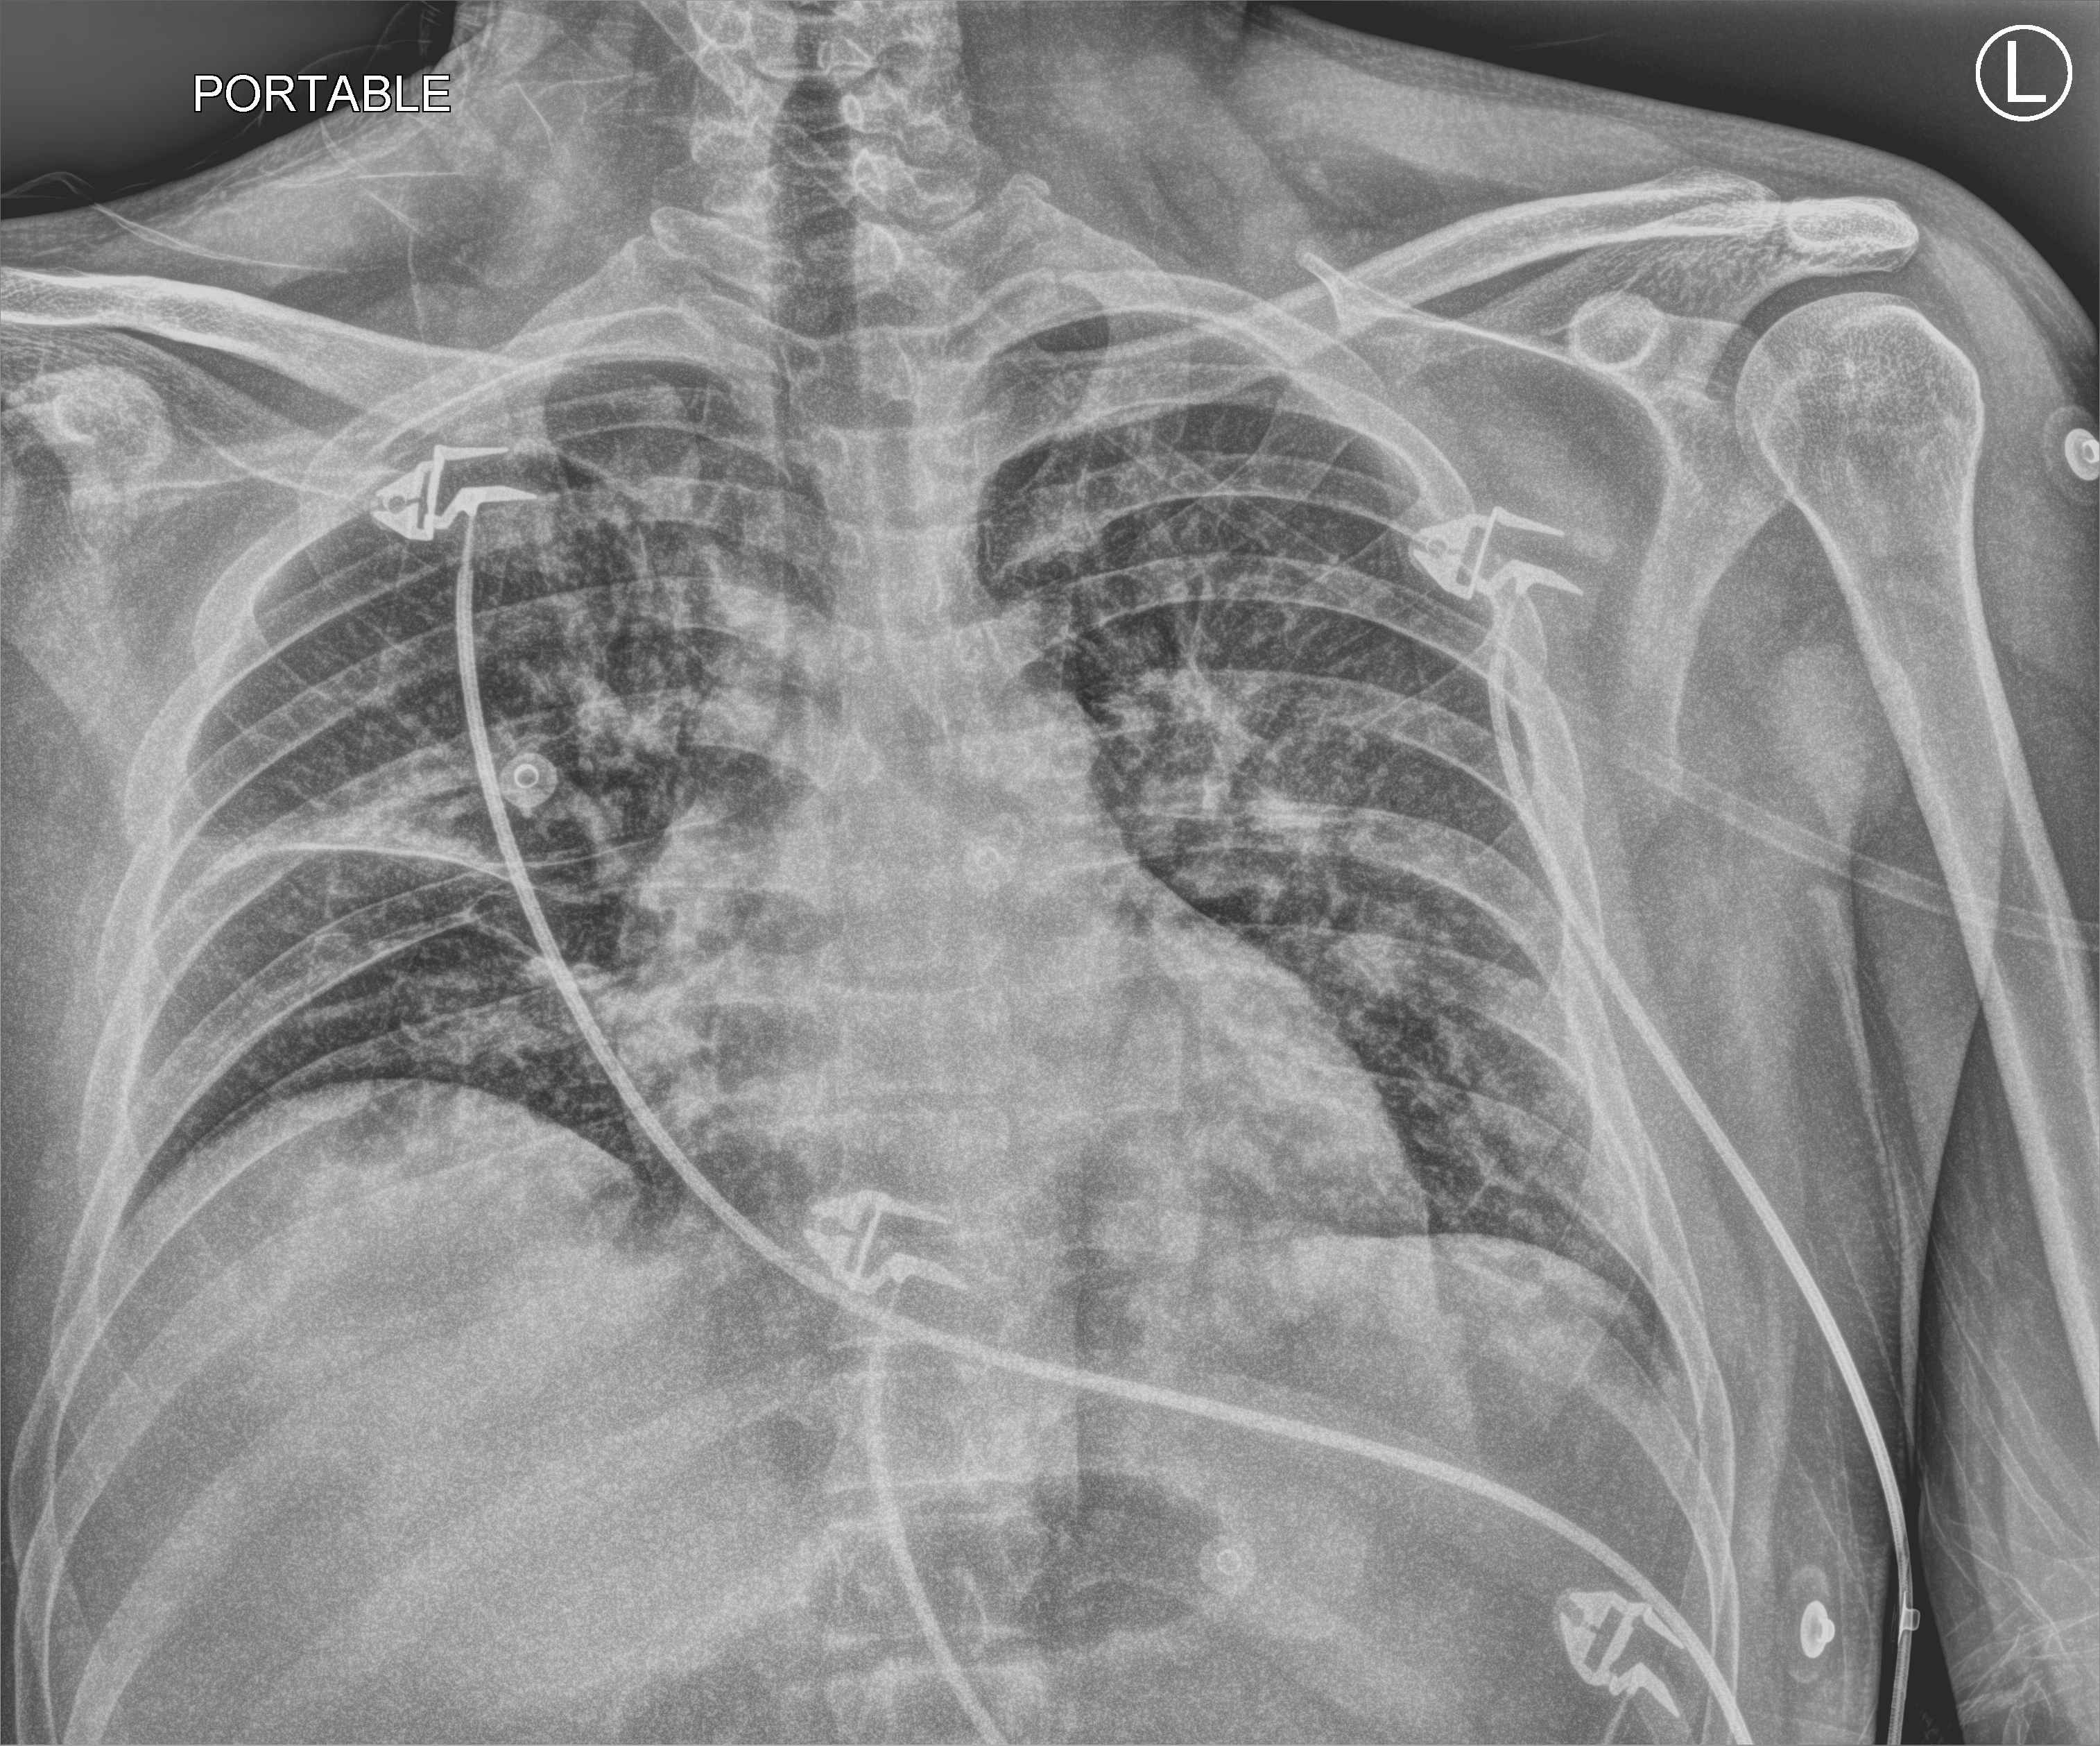
Bedside chest radiograph (computed radiography). Patient hospitalised with COVID-19, aged 18–59 years.
Hospital-stay facts (about this admission, not read from this image; timing relative to this image not recorded): admitted to intensive care during this hospital stay: yes.